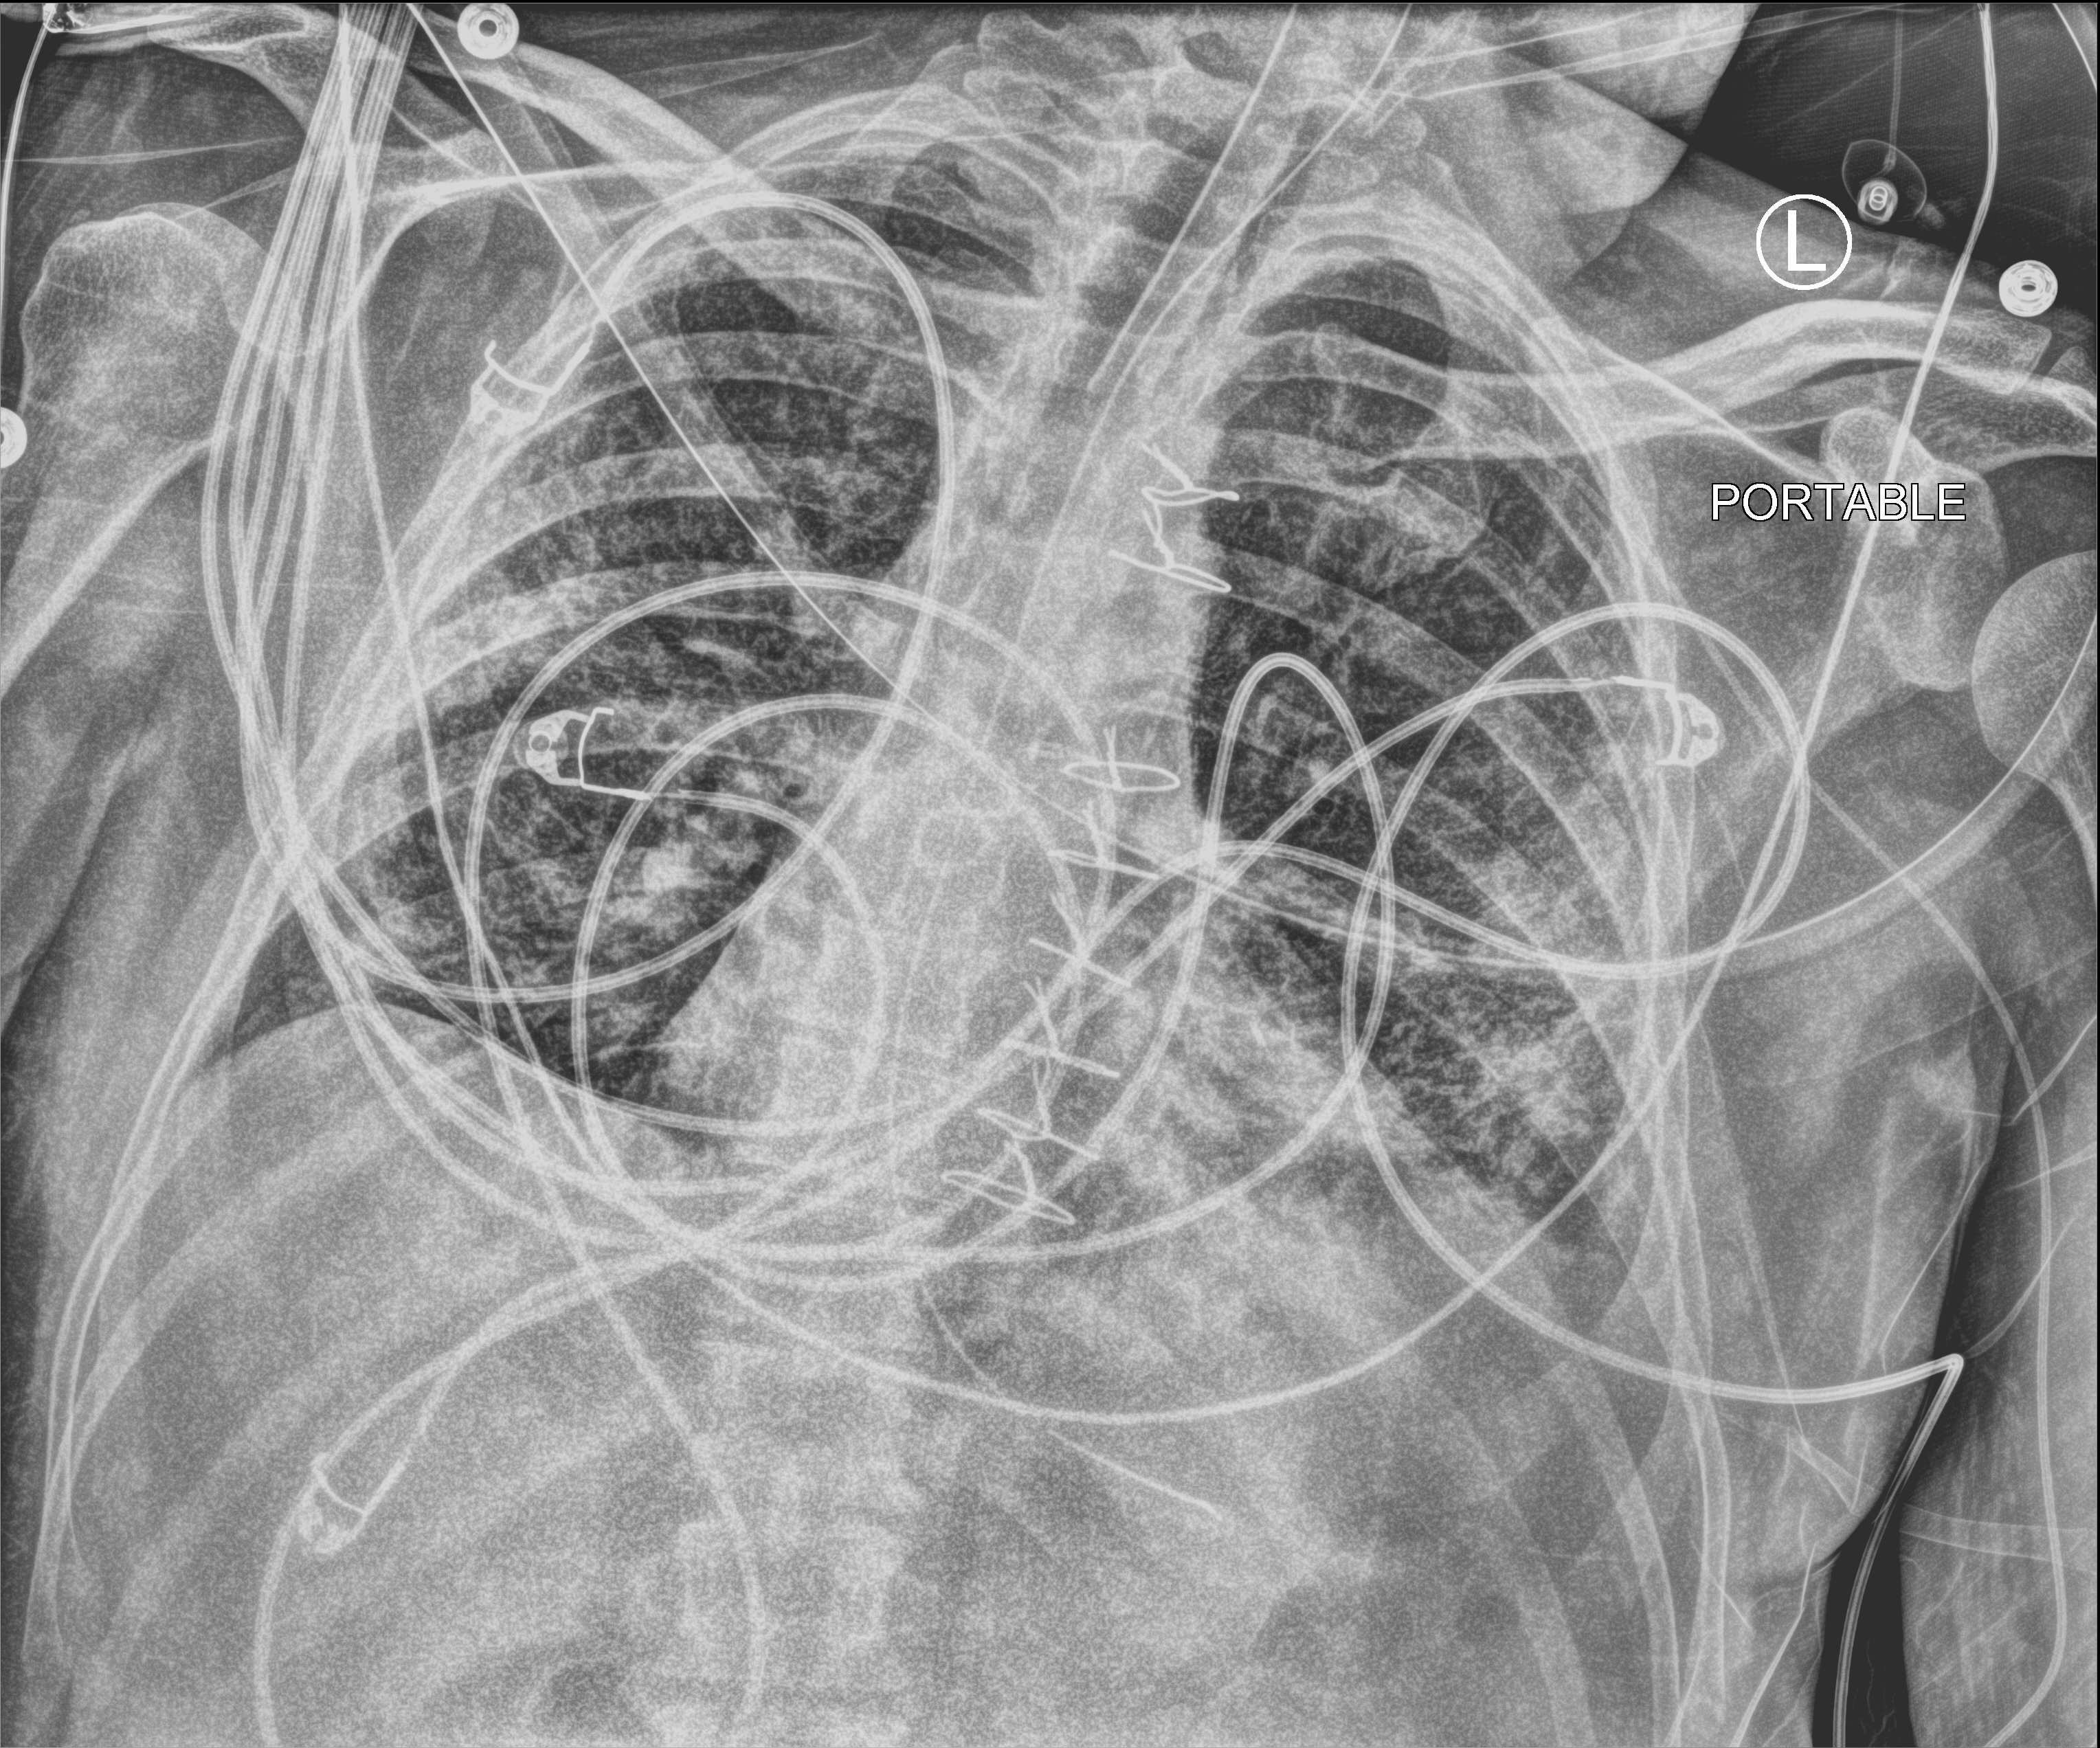
Bedside chest radiograph (computed radiography), anteroposterior (AP) projection. Patient hospitalised with COVID-19; male, aged 18–59 years.
Admission-level facts for this patient (not findings on this image; timing relative to this image not recorded): mechanically ventilated during this hospital stay: yes; chronic kidney disease (admission record): no; admitted to intensive care during this hospital stay: yes.